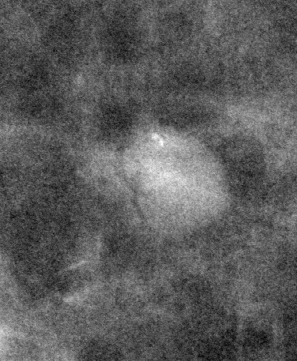
Crop from a digitized film mammogram around one marked abnormality; right breast; CC view; BI-RADS breast density category 1 (scale 1–4).
Finding: calcifications, morphology punctate, distribution clustered; BI-RADS assessment category 4; subtlety rating 5 on a 1 (subtle) to 5 (obvious) scale; pathology (as recorded): benign.